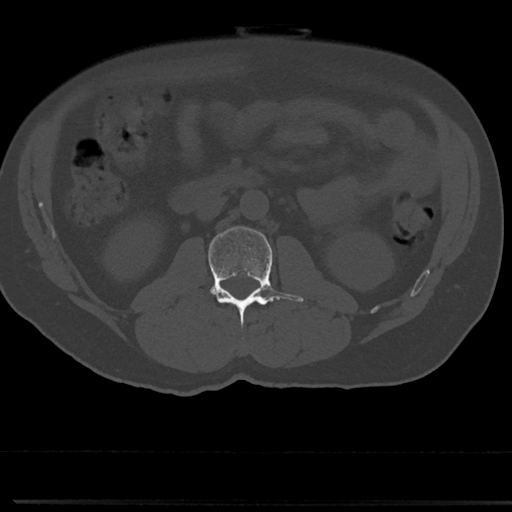
CT including the spine, one axial slice; slice 12 of 817 in the series (ordered by position); reconstruction kernel Br40s/3; 120 kVp; bone window (W 1800 / L 400 HU); 0.5 mm slice thickness; 512 × 512 image matrix. Male patient, age 61 years. Case-level facts recorded for this patient, not image findings: primary cancer: prostate.
Structures marked on this image (semi-automatic segmentation, software-assisted and operator-edited):
- L2 vertebra: box from (x=208, y=226) to (x=303, y=343) px